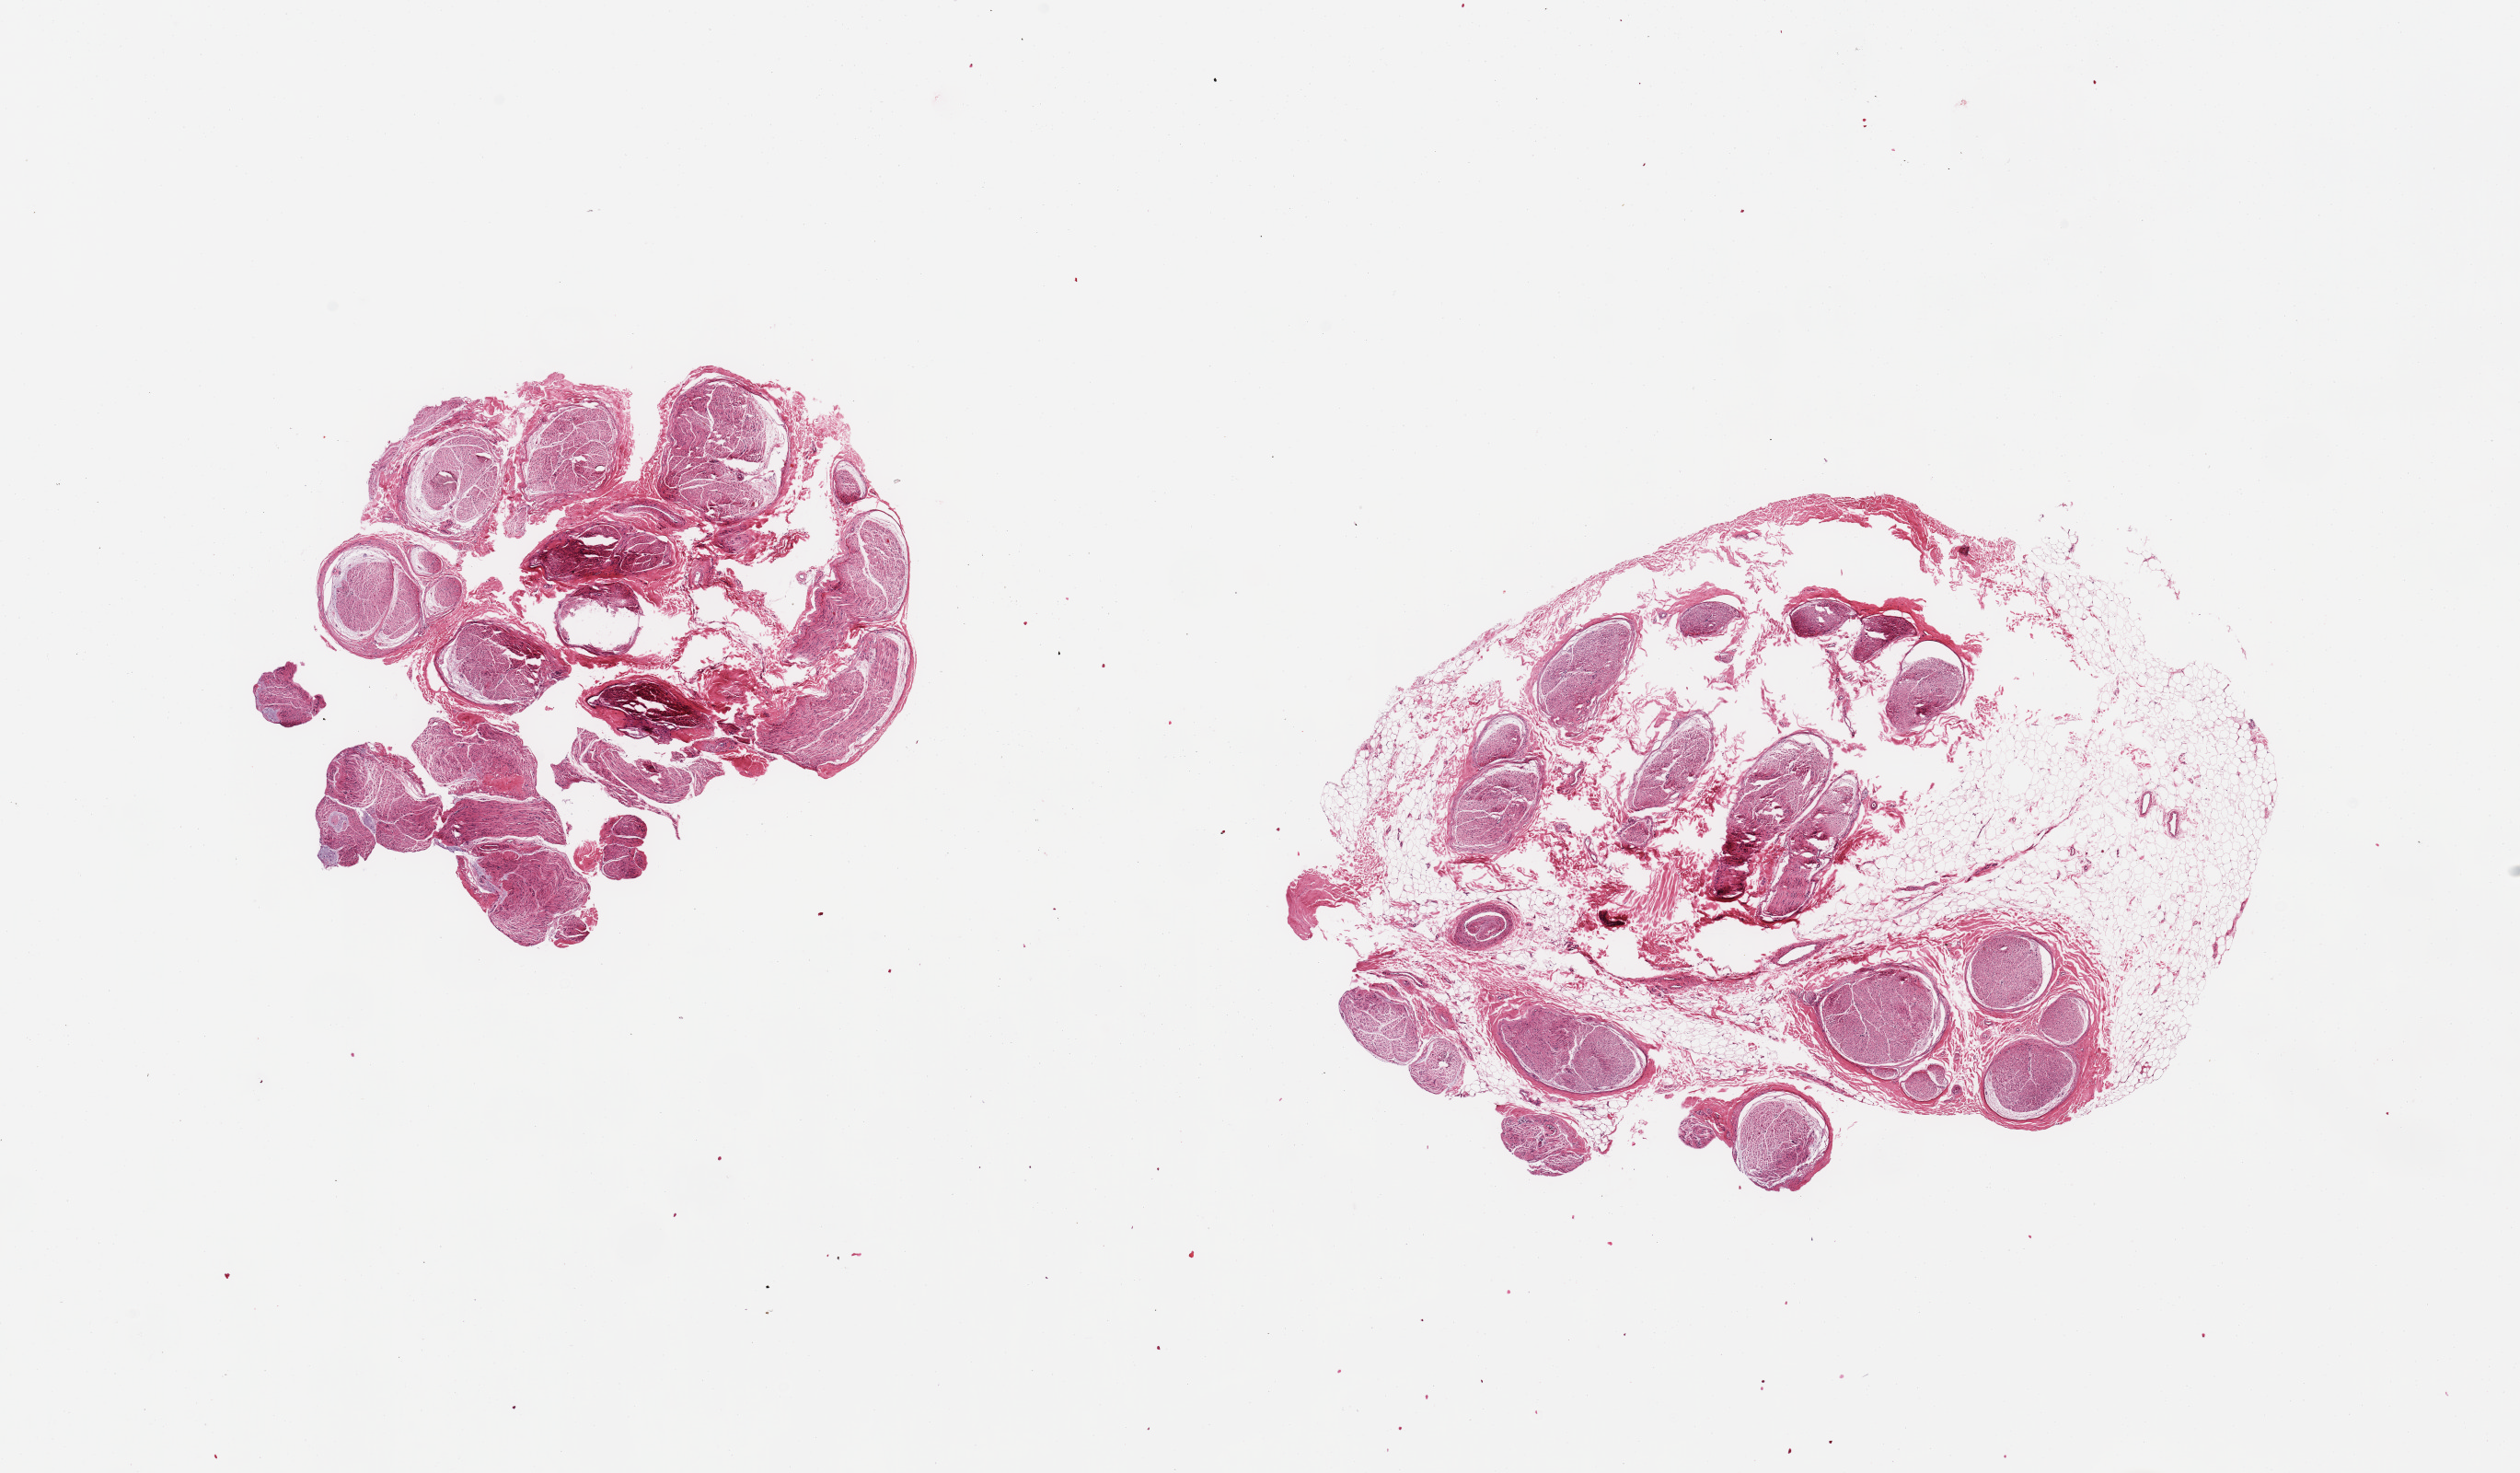
H&E whole-slide image — whole scanned area (about 21.7 x 12.7 mm, from a 20x scan) shown as a low-resolution overview; PAXgene-fixed, paraffin-embedded tissue; section of tibial nerve (target tissue); tissue donor sample. Donor: male.
Review note (as recorded): 2 fragmented pieces; 30% fat.